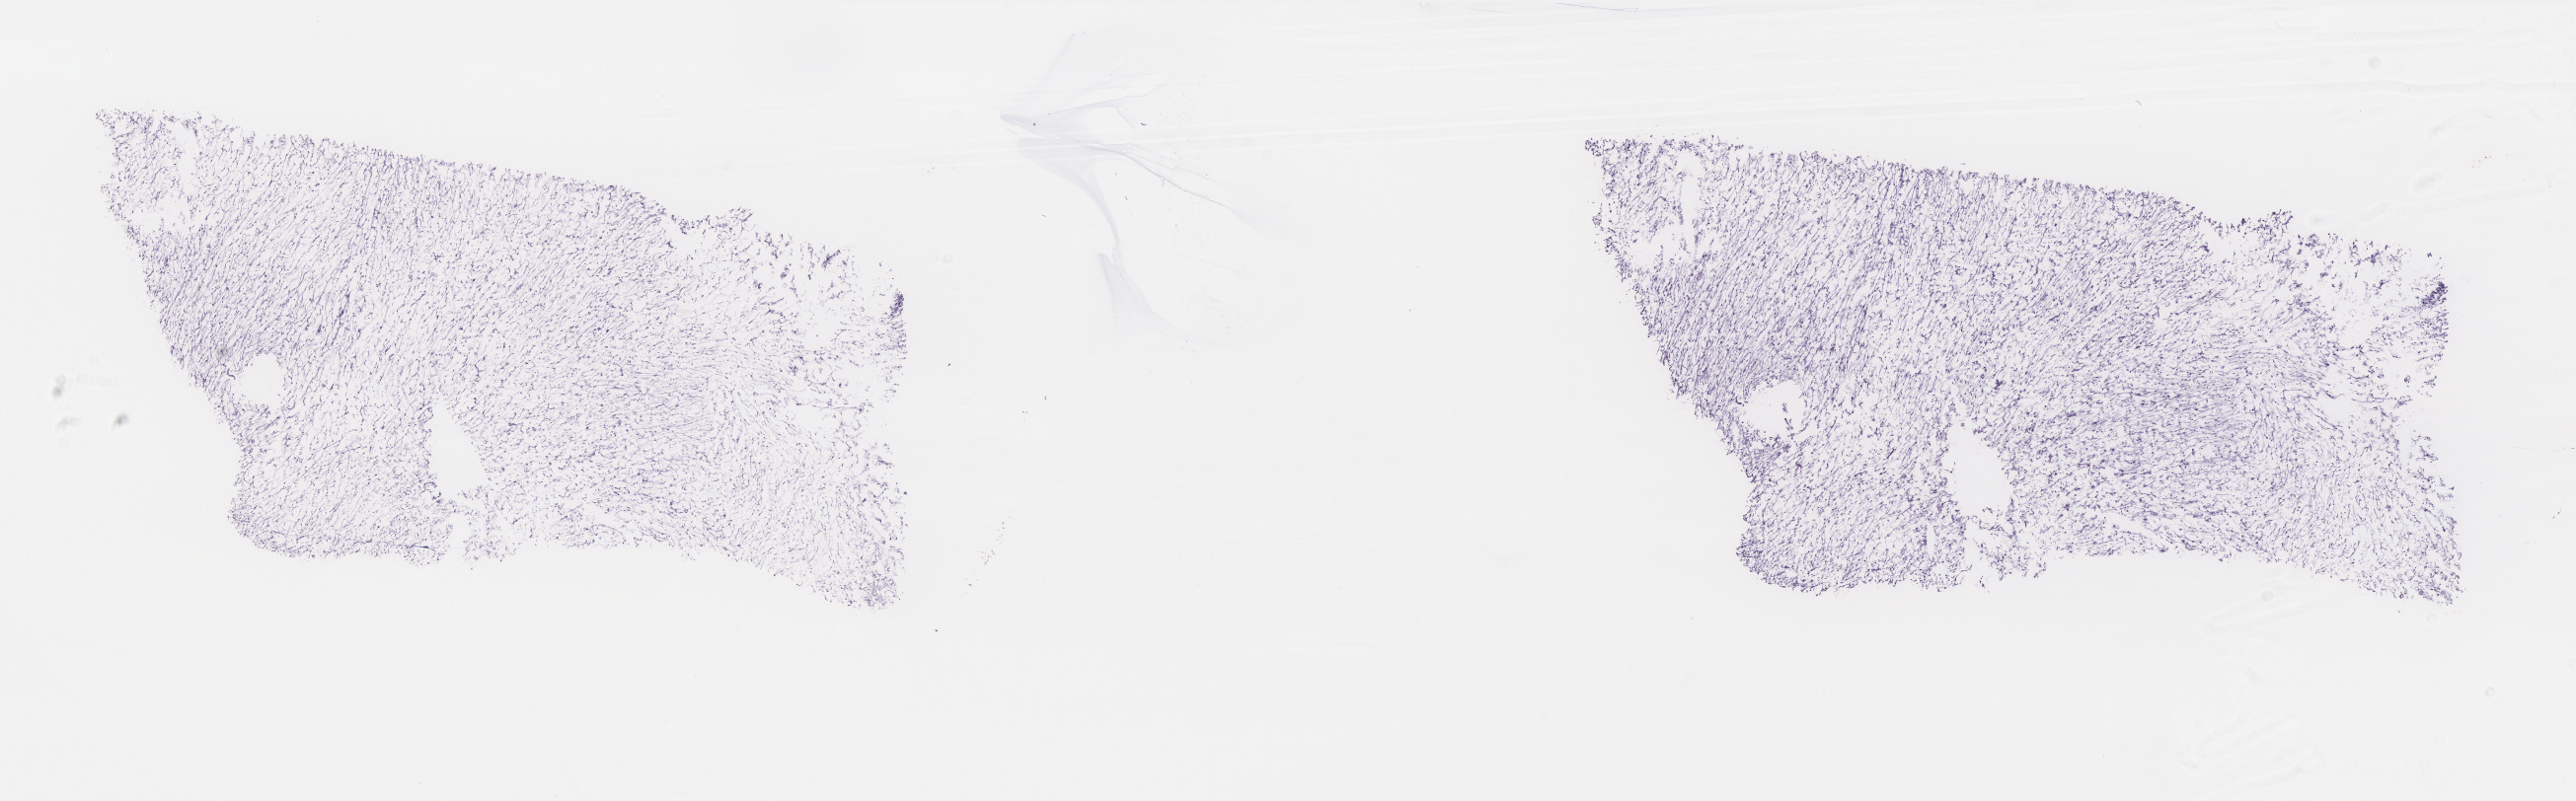
Whole-slide histology image, Hematoxylin and eosin (H&E) stained, a low-resolution overview of the entire scanned area, about 20.9 x 6.5 mm (acquisition: 40x scan), frozen section from the top of the tissue portion, primary tumour sample from the retroperitoneum and peritoneum. Male patient; age at initial diagnosis 78 years. Composition of this section per pathologist review: tumour cells 85%, tumour nuclei 85%, normal cells 0%, stromal cells 15%, necrosis 0%. Inflammatory infiltration, as recorded: lymphocyte infiltration 2%, monocyte infiltration 1%, neutrophil infiltration 1%.
Diagnosis: Dedifferentiated liposarcoma (retroperitoneum).